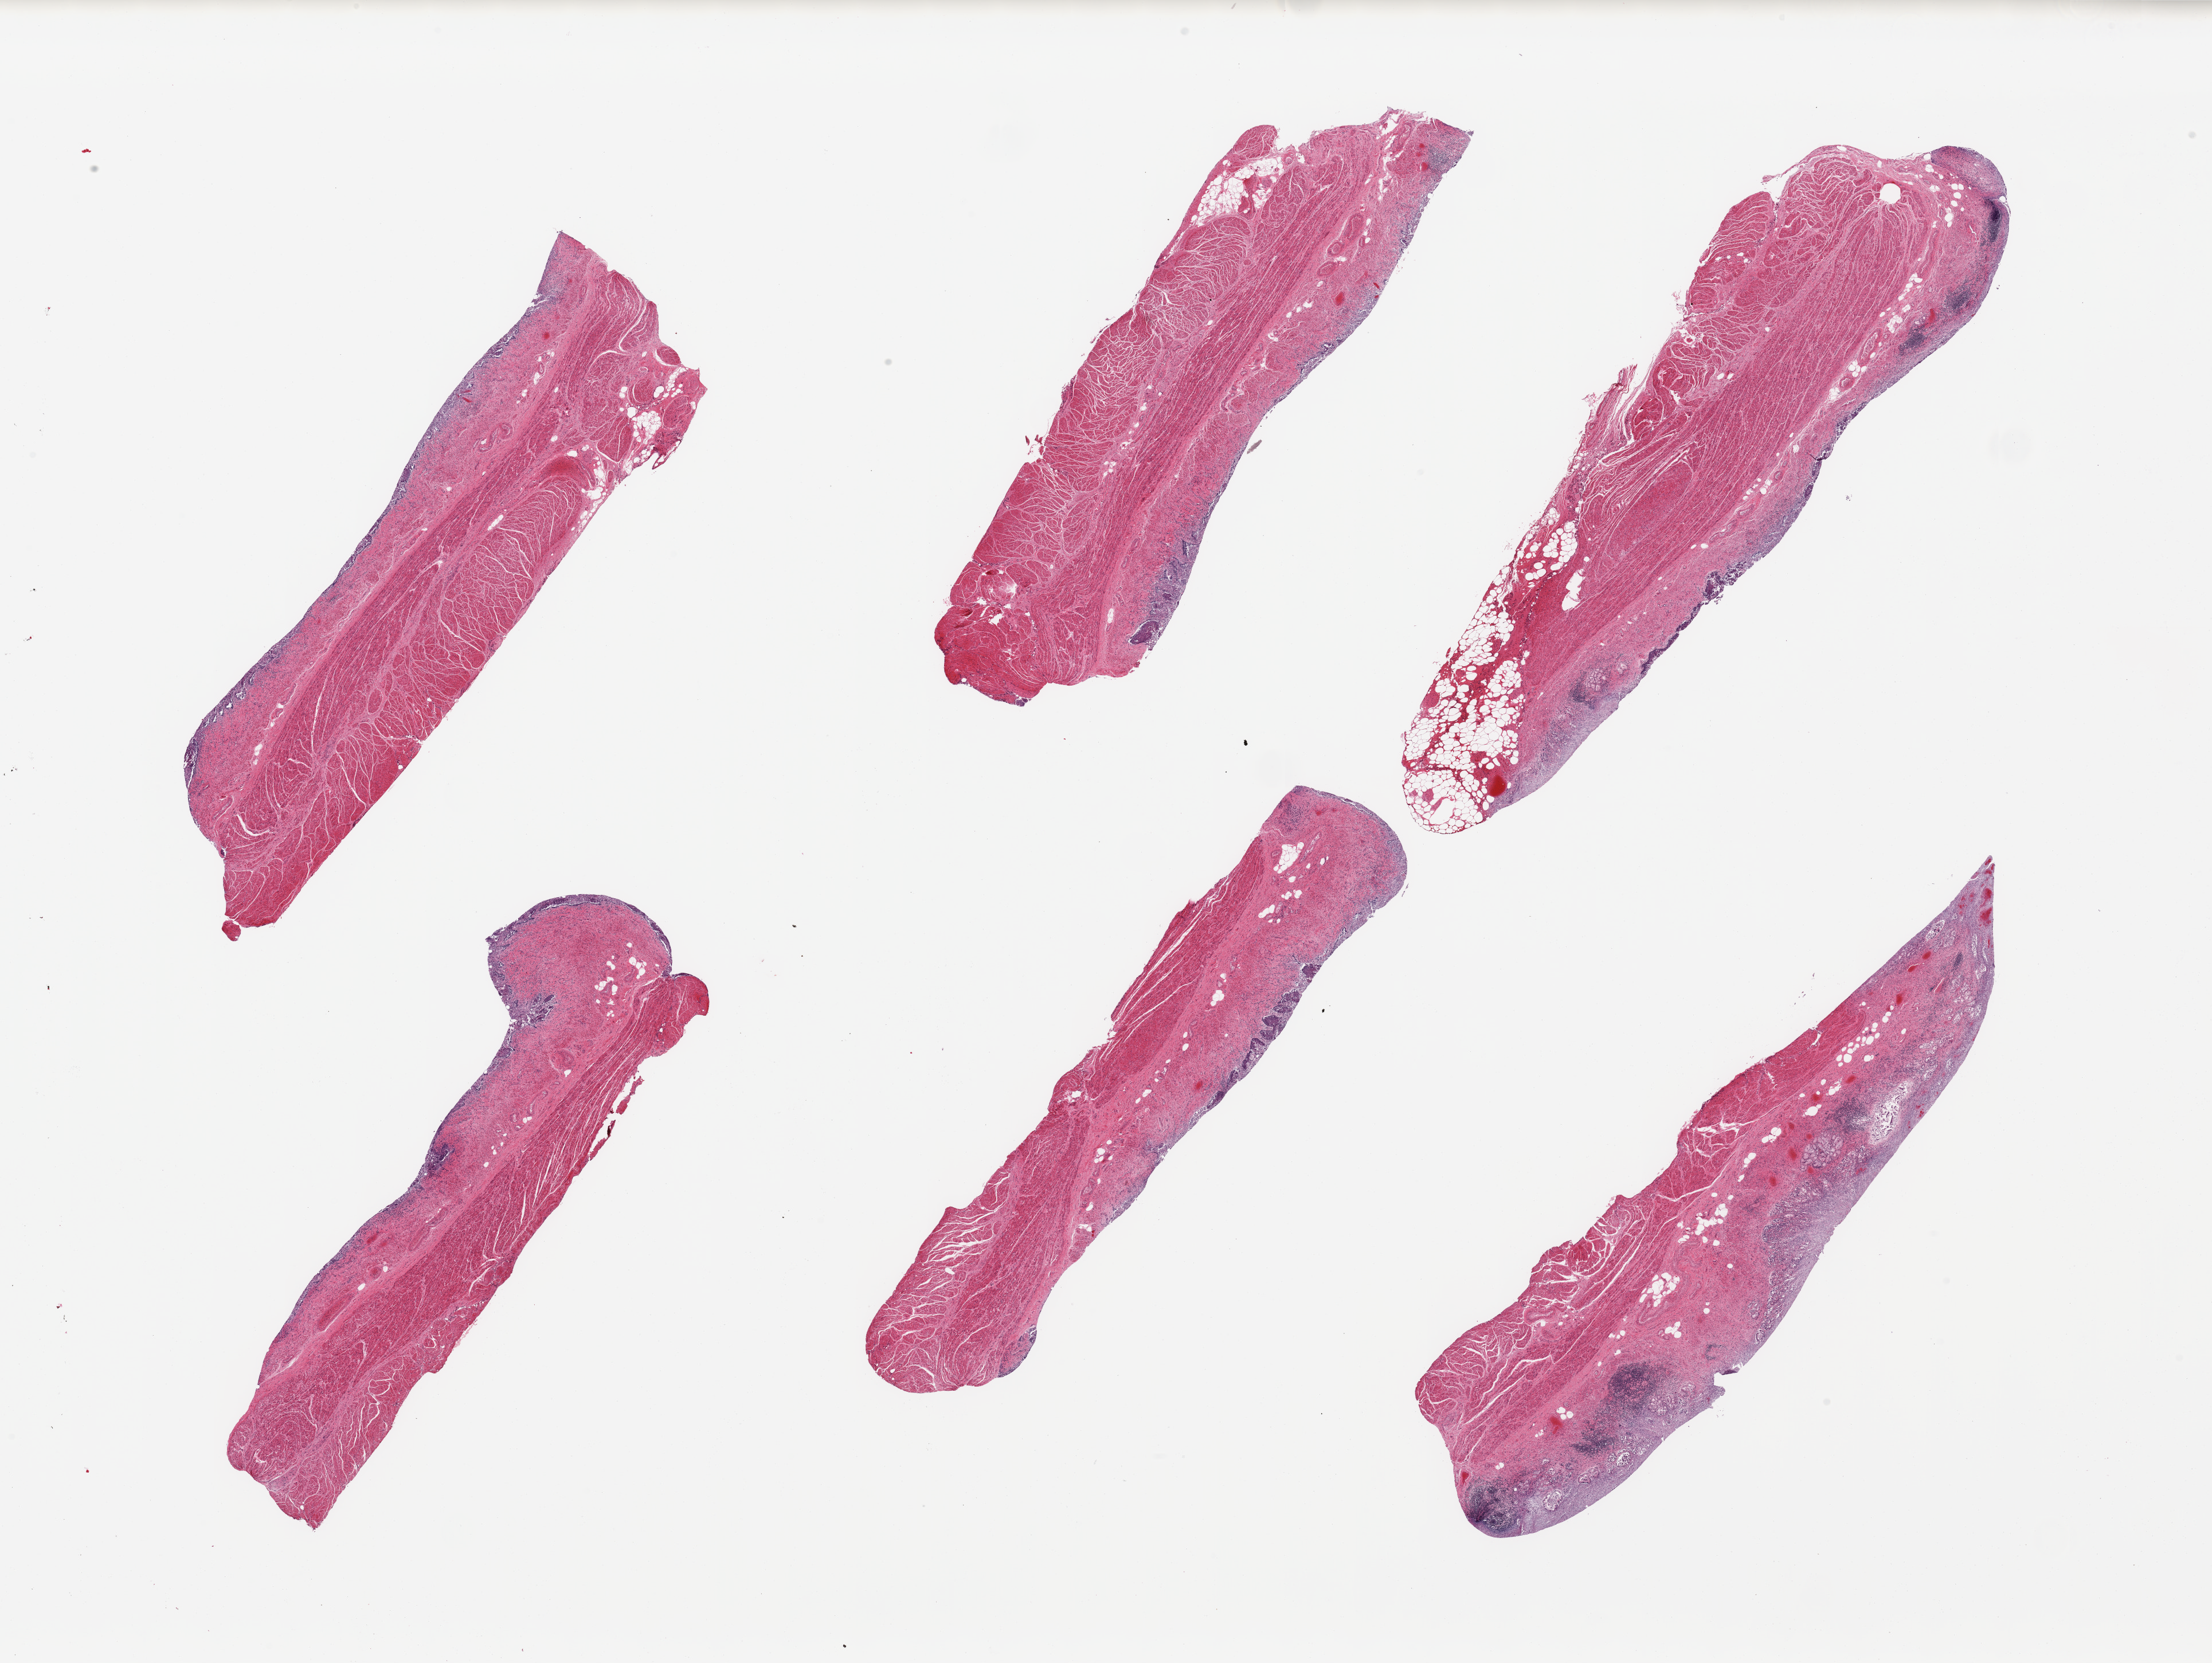
Digitized hematoxylin and eosin (H&E)-stained section, shown as a low-resolution overview of the whole scanned area (about 30.5 x 22.9 mm, slide scanned at 20x). PAXgene-fixed, paraffin-embedded tissue. Sampled site (target tissue): gastroesophageal junction. Tissue donor sample. Male donor.
- pathologist's review note for this sample: 6 pieces; target muscularis, present, ~10% contaminat completely autolyzed mucosa